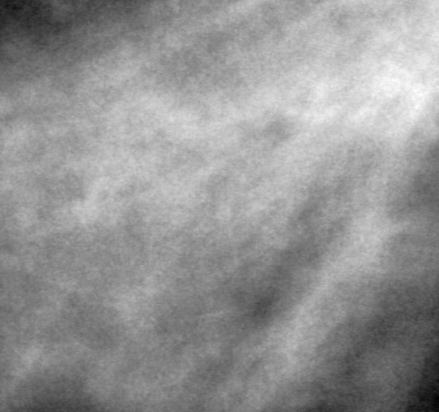
Cropped region of a digitized screen-film mammogram centred on a radiologist-marked abnormality; right breast; CC view; BI-RADS breast density category 3 (scale 1–4).
Mass, shape round, margins obscured; BI-RADS assessment category 4; pathology (as recorded): benign.